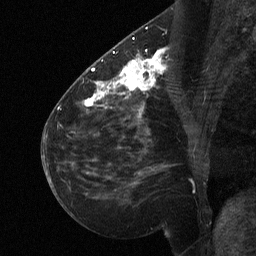
Breast MRI (dynamic contrast-enhanced), one sagittal slice; position 29 of 64 along the scan axis; dynamic contrast-enhanced study with each time point stored as its own series, time point 2 of 3 at this slice position (early post-contrast, ordered by acquisition time); 1.5 T; TE 4.8 ms, TR 27 ms; 2 mm slice thickness; 256 × 256 image matrix, field of view 200 × 200 mm. Patient: female, 51 years. Case-level facts recorded for this patient, not image findings: setting: breast cancer imaged before/during neoadjuvant chemotherapy; receptor status: HR-positive, HER2-negative.
Outlined on this slice (semi-automatically segmented with operator editing):
- analysis volume of interest (the breast-tissue region the enhancement analysis was run in; not a lesion): bounding box (x1, y1, x2, y2) in pixels: (112, 46, 169, 106)
- tumour enhancement mask (voxels above the 90 % enhancement threshold inside the analysis volume of interest): (112, 53, 166, 93)